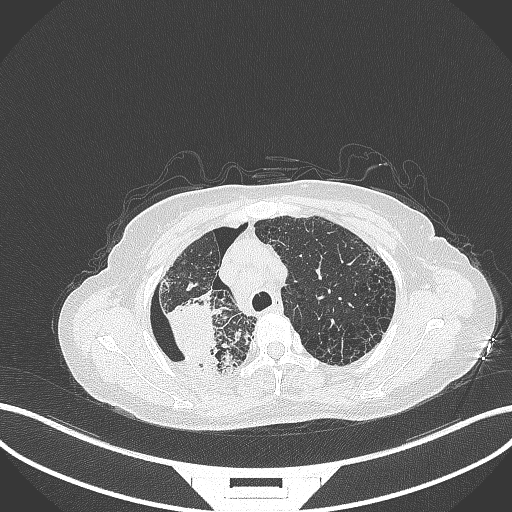
Chest CT, one axial slice; position 275 of 408 along the scan axis; reconstruction kernel B70f; 120 kVp; lung window (W 1500 / L -600 HU); 1 mm slice thickness; 512 × 512 image matrix. Patient: female, 64 years. Case-level facts recorded for this patient, not image findings: clinical TNM (as recorded): T3 N3 M0.
Annotated regions visible in this slice (rectangle marked by the reading radiologist):
- lung tumour (recorded histology: squamous cell carcinoma): box from (x=163, y=296) to (x=223, y=366) px